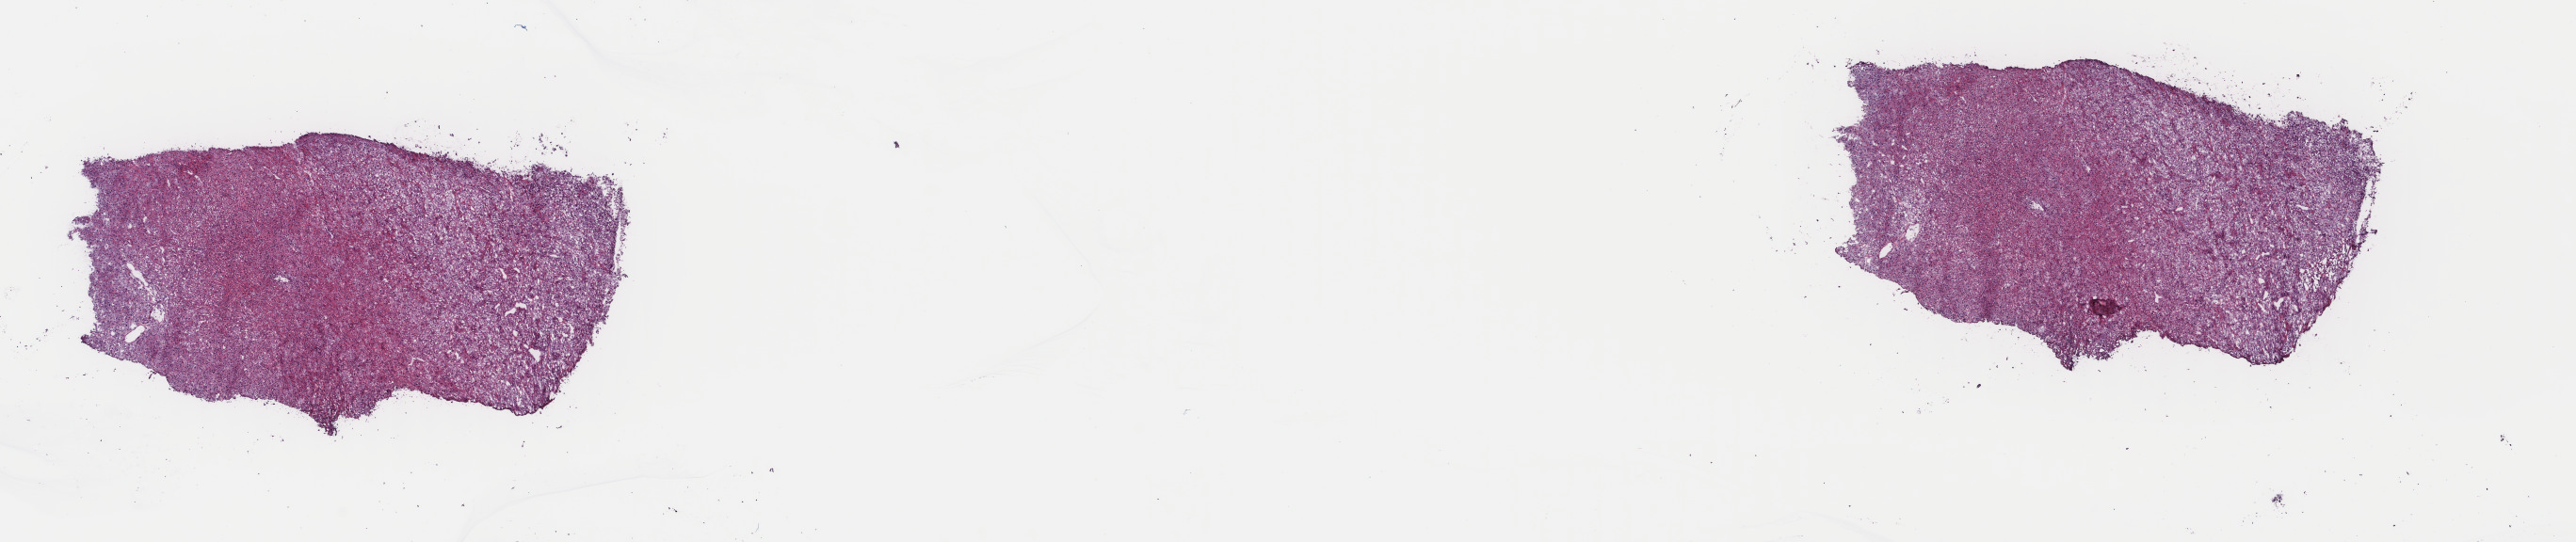
Whole-slide histology image, H&E — whole scanned area (about 21.7 x 4.6 mm) shown as a low-resolution overview. Frozen section. Adrenal cortex, primary tumour sample. Patient: female, age at initial diagnosis 58 years. Composition of this section per pathologist review: tumour cells 85%, tumour nuclei 85%.
Pathologic diagnosis: Adrenal cortical carcinoma (cortex of adrenal gland).